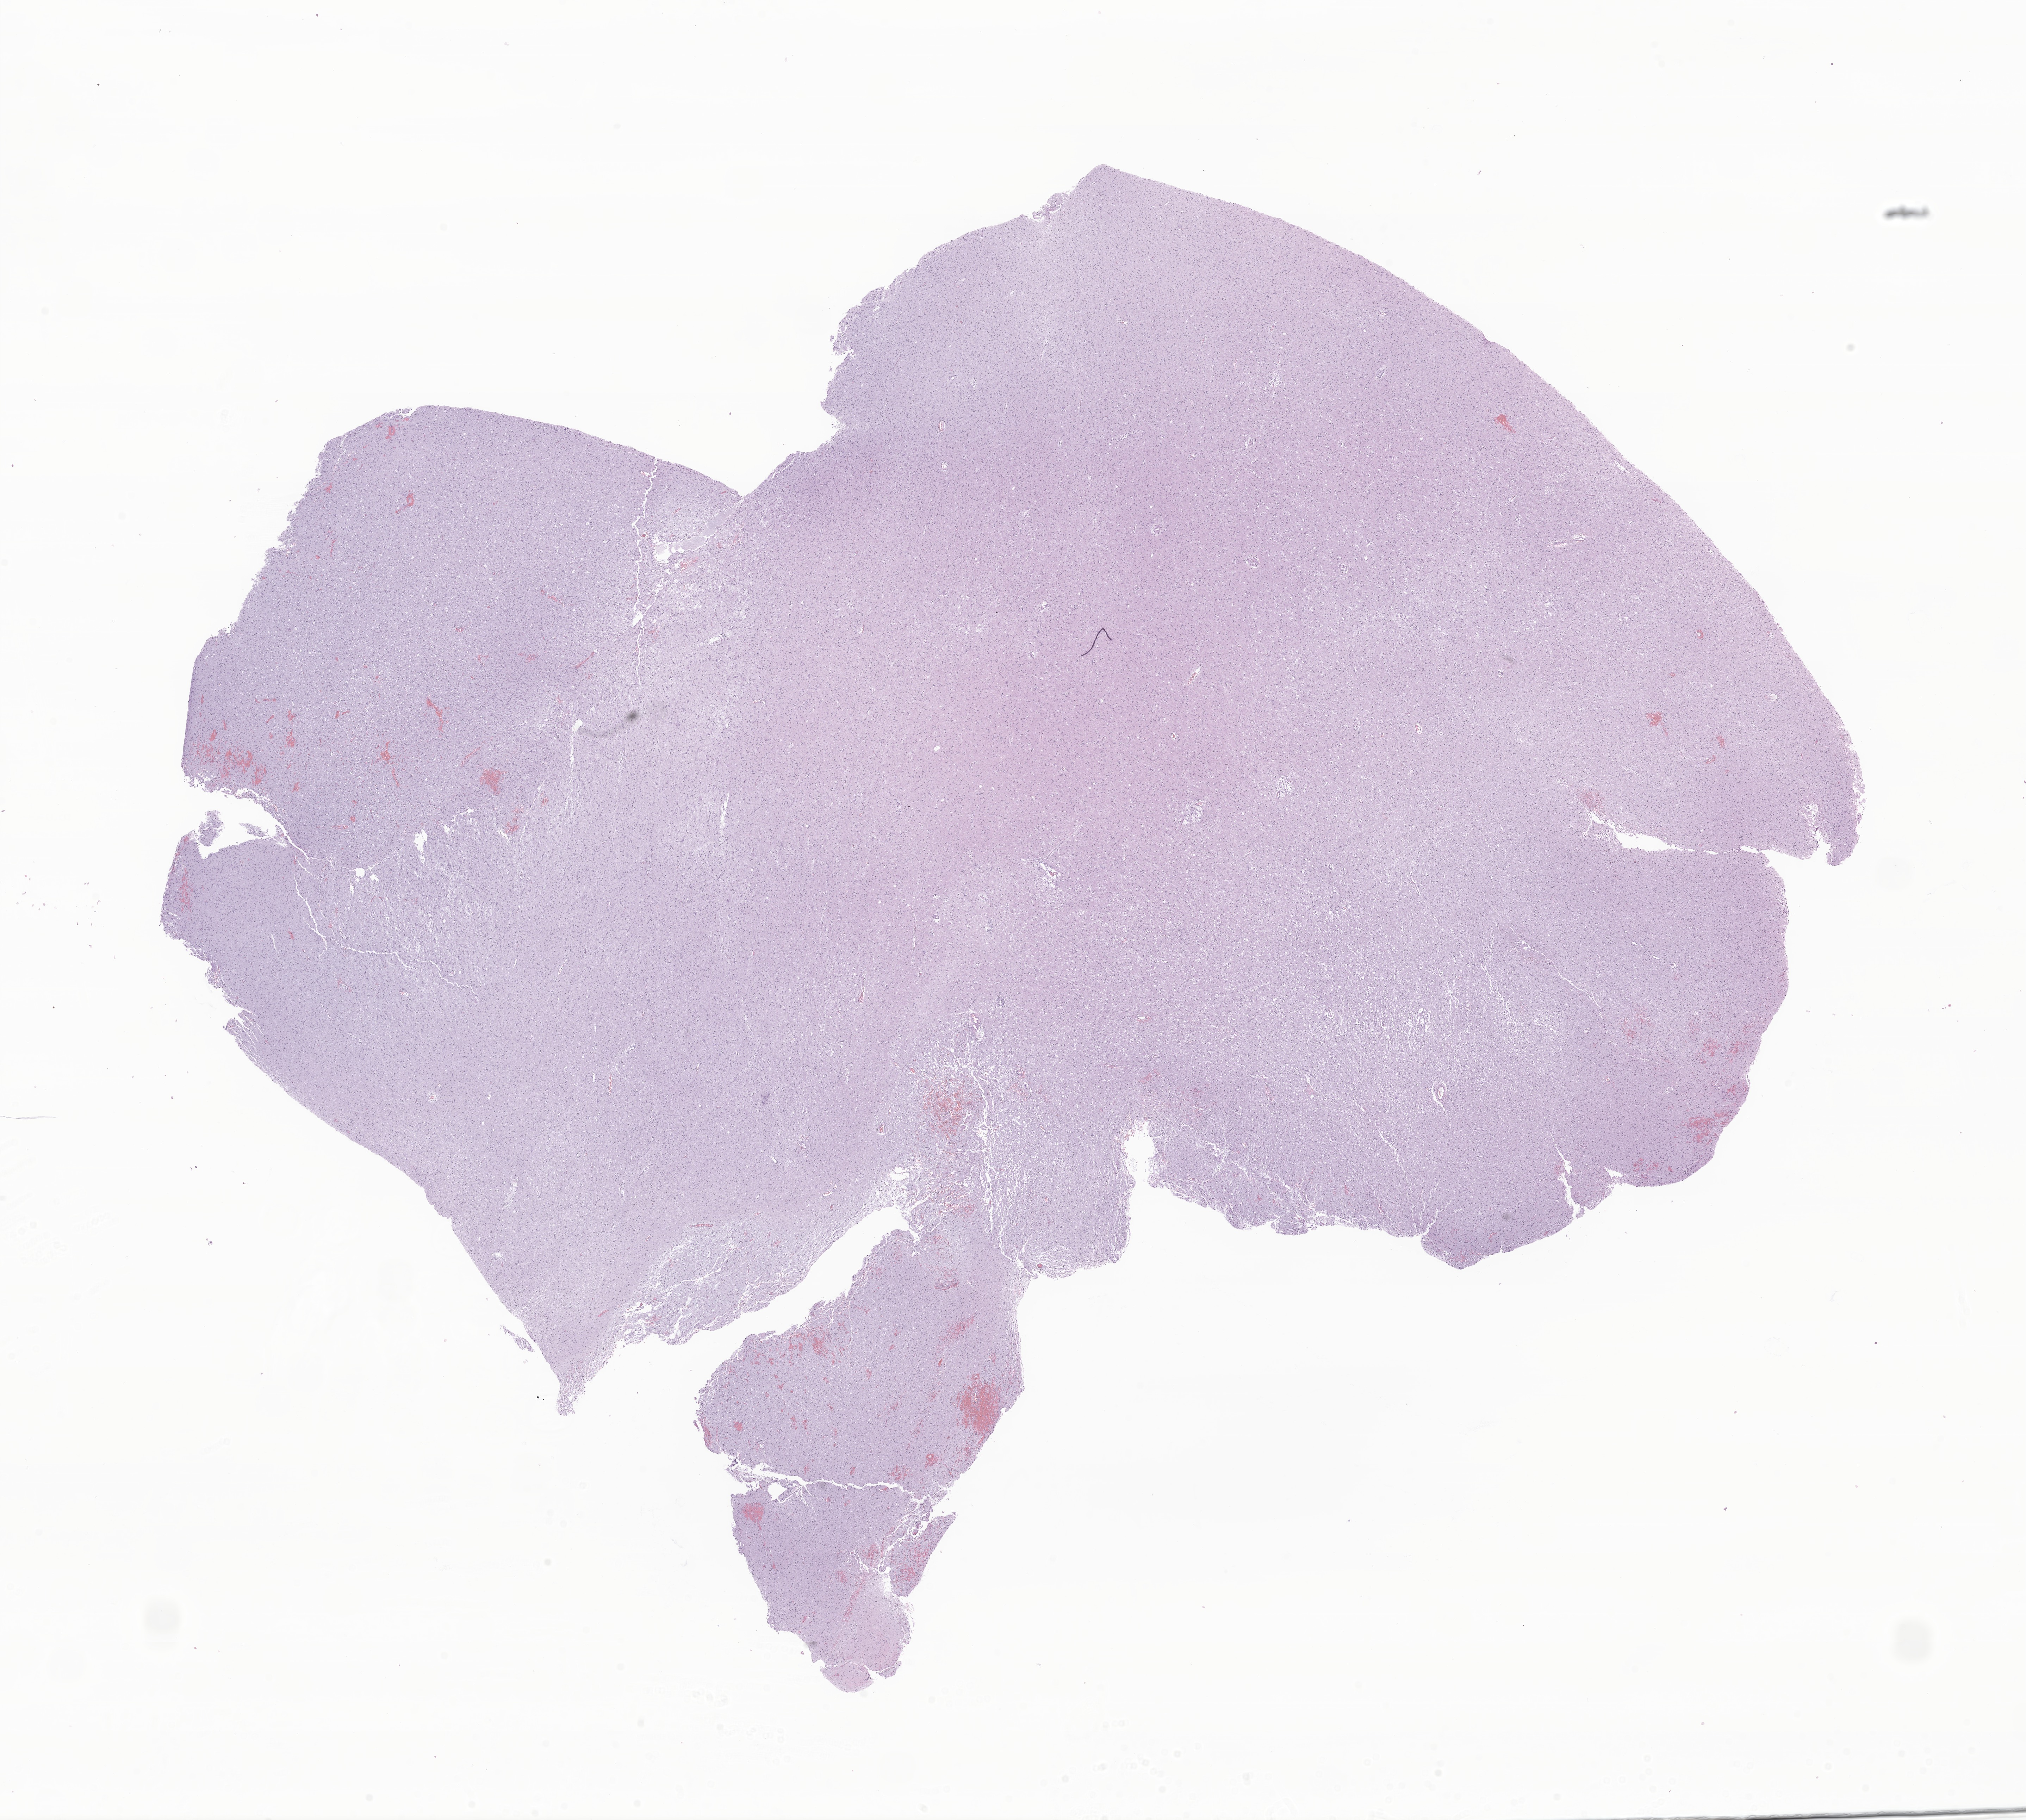
Whole-slide image, H&E stain of tumor tissue from the brain, low-resolution overview of the scanned area, about 24.2 x 21.8 mm, formalin-fixed, paraffin-embedded (FFPE) tissue. Male patient, age 163 months (13 years 7 months).
Recorded diagnosis: Neoplasm, malignant.